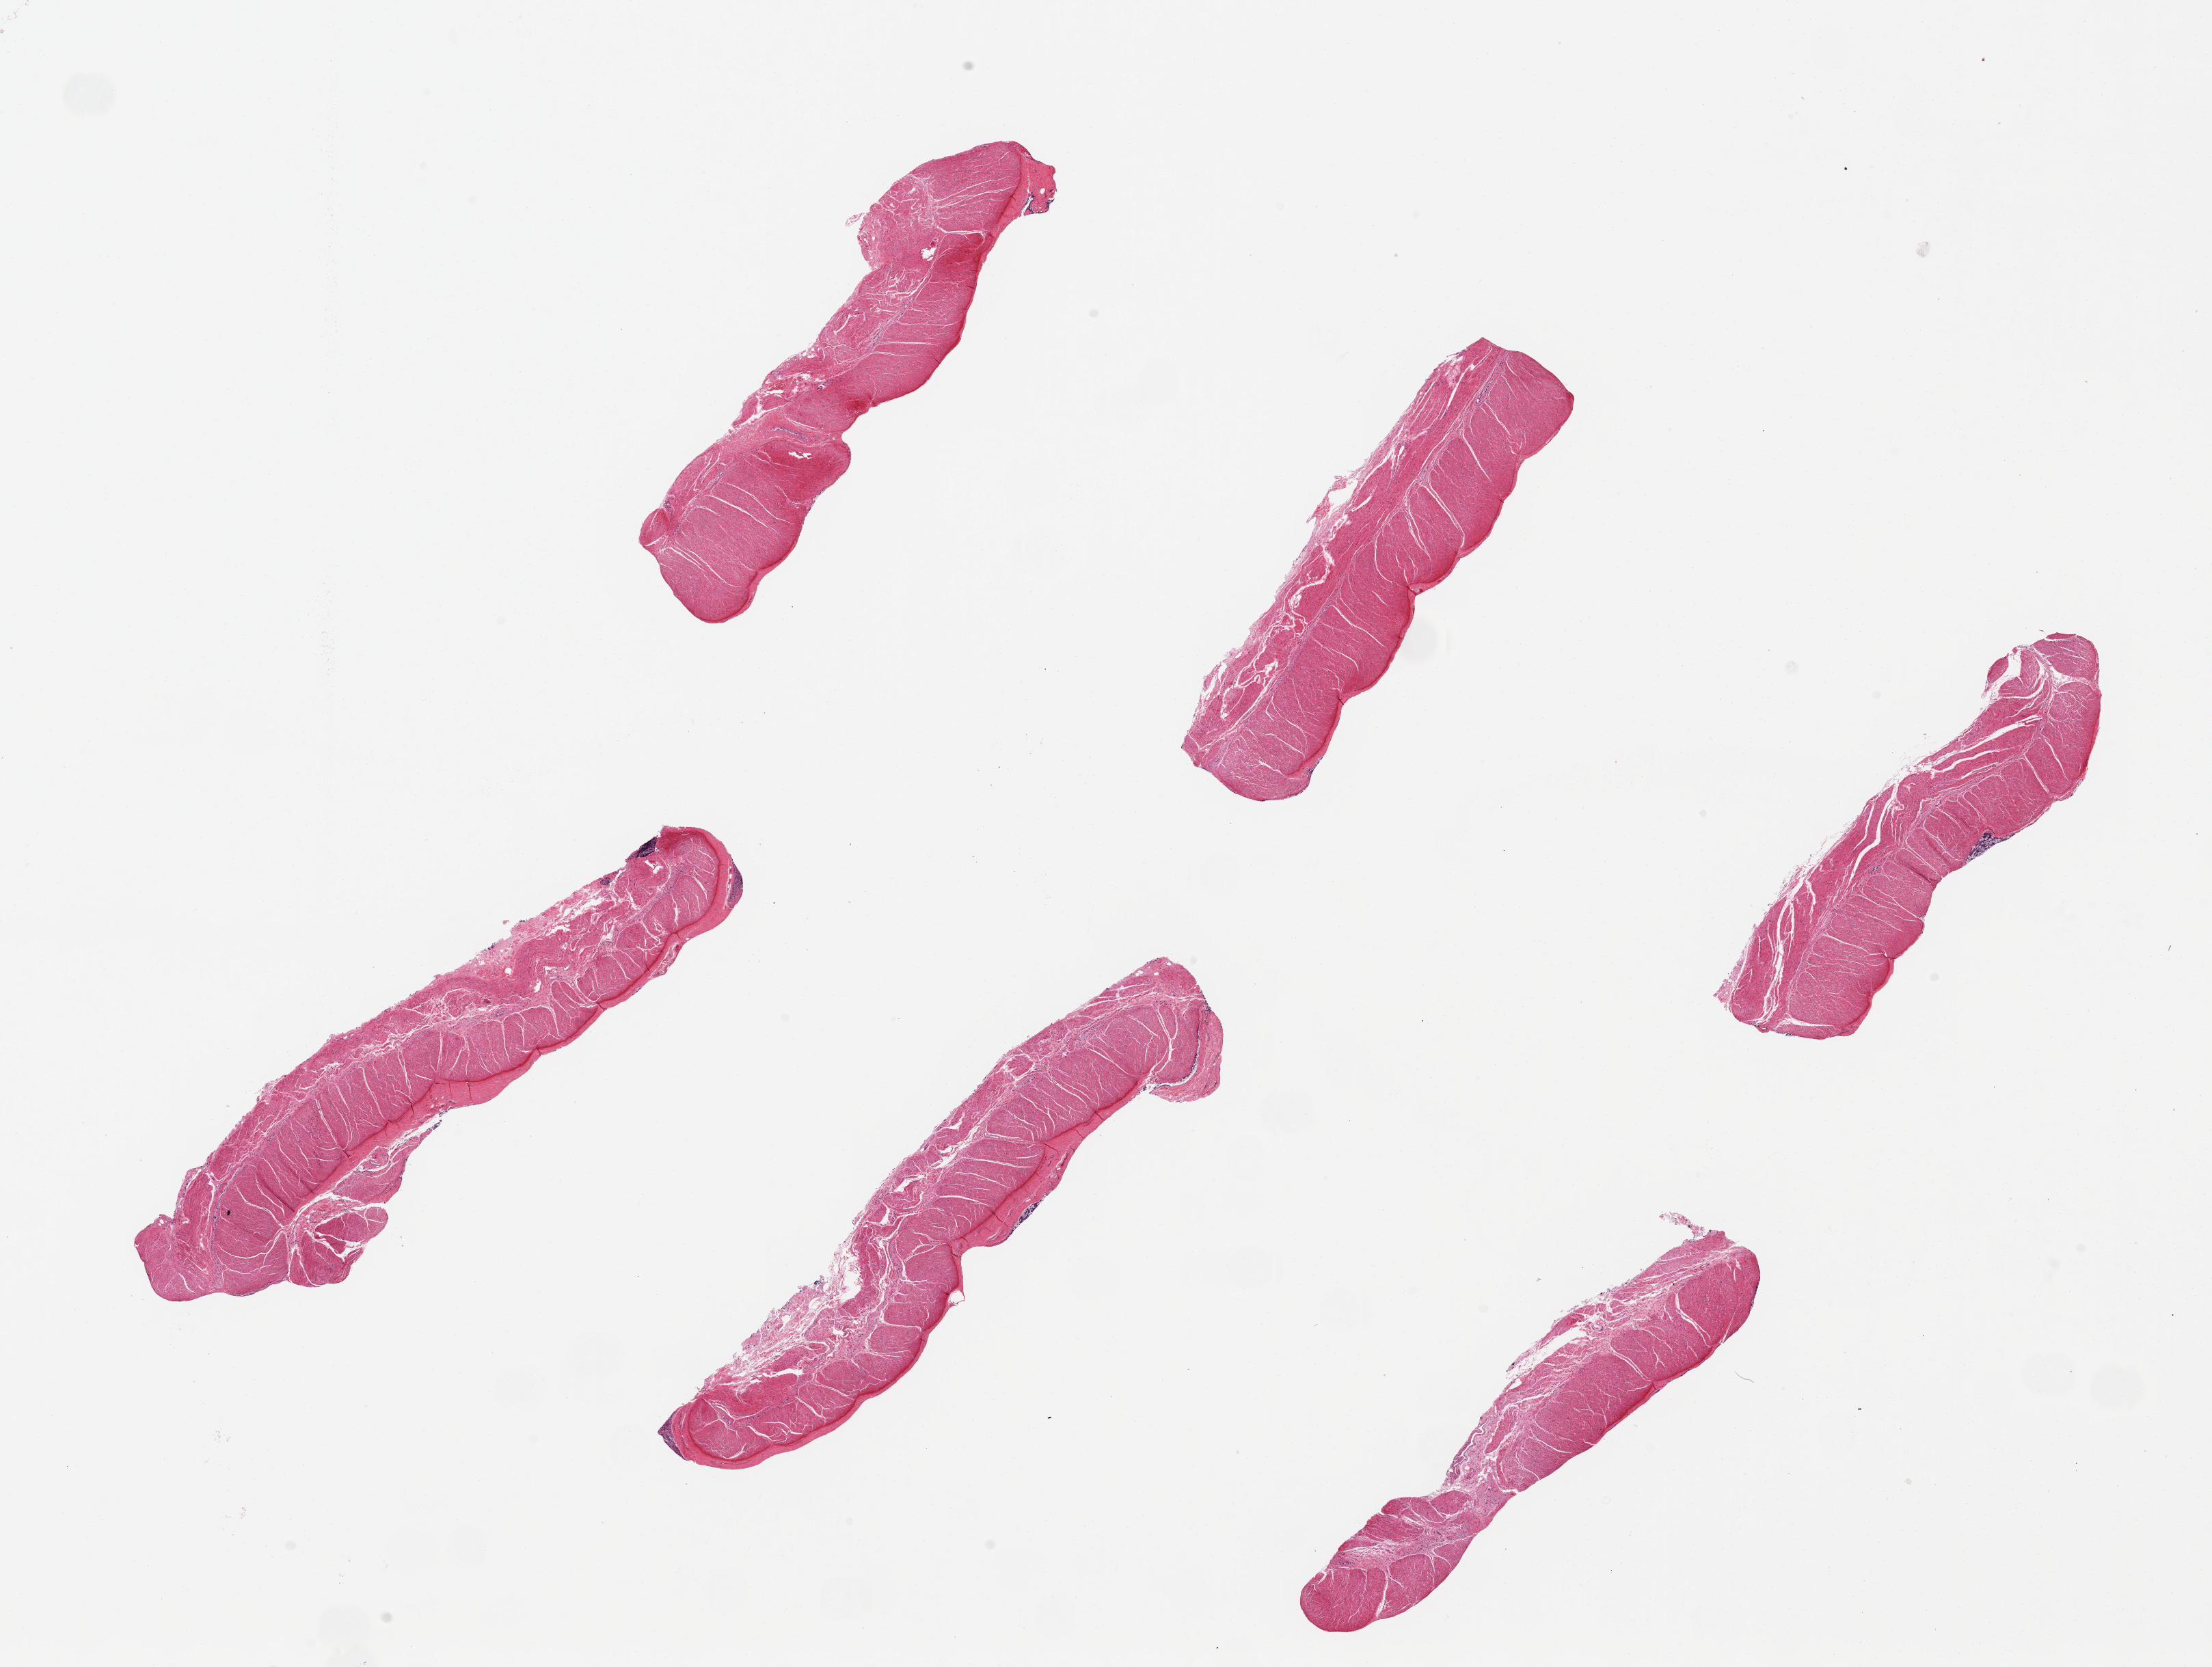
Digitized hematoxylin and eosin (H&E)-stained section, brightfield — shown as a low-resolution overview of the whole scanned area (about 25.6 x 19.3 mm, from a 20x scan), PAXgene-fixed, paraffin-embedded tissue, section of sigmoid colon (target tissue), donor tissue sample. Donor sex: female.
* reviewer comment on this tissue sample: 6 pieces, up to 8x2mm; virtually all muscle as targeted; minute focal mucosa in 2 pieces